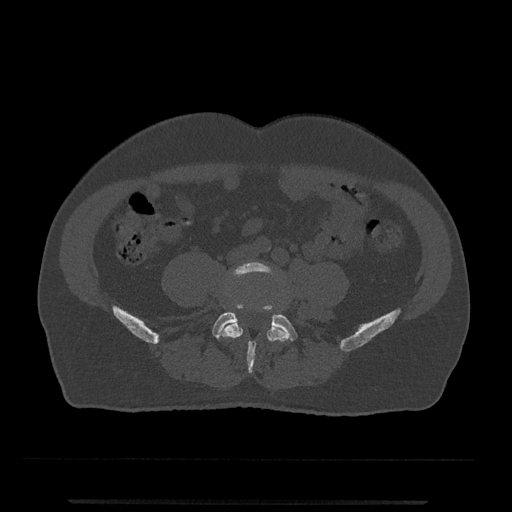
CT including the spine, one axial slice. Slice 100 of 797 in the series (ordered by position). Bone window (W 1800 / L 400 HU). 0.5 mm slice thickness. 512 × 512 image matrix, field of view 419 × 419 mm. Patient: male, 63 years. From the clinical record (not read from this slice): primary cancer: prostate.
Outlined on this slice (semi-automatically segmented with operator editing):
- L4 vertebra: bounding box (x1, y1, x2, y2) in pixels: (220, 261, 289, 370)
- L5 vertebra: (212, 305, 298, 371)